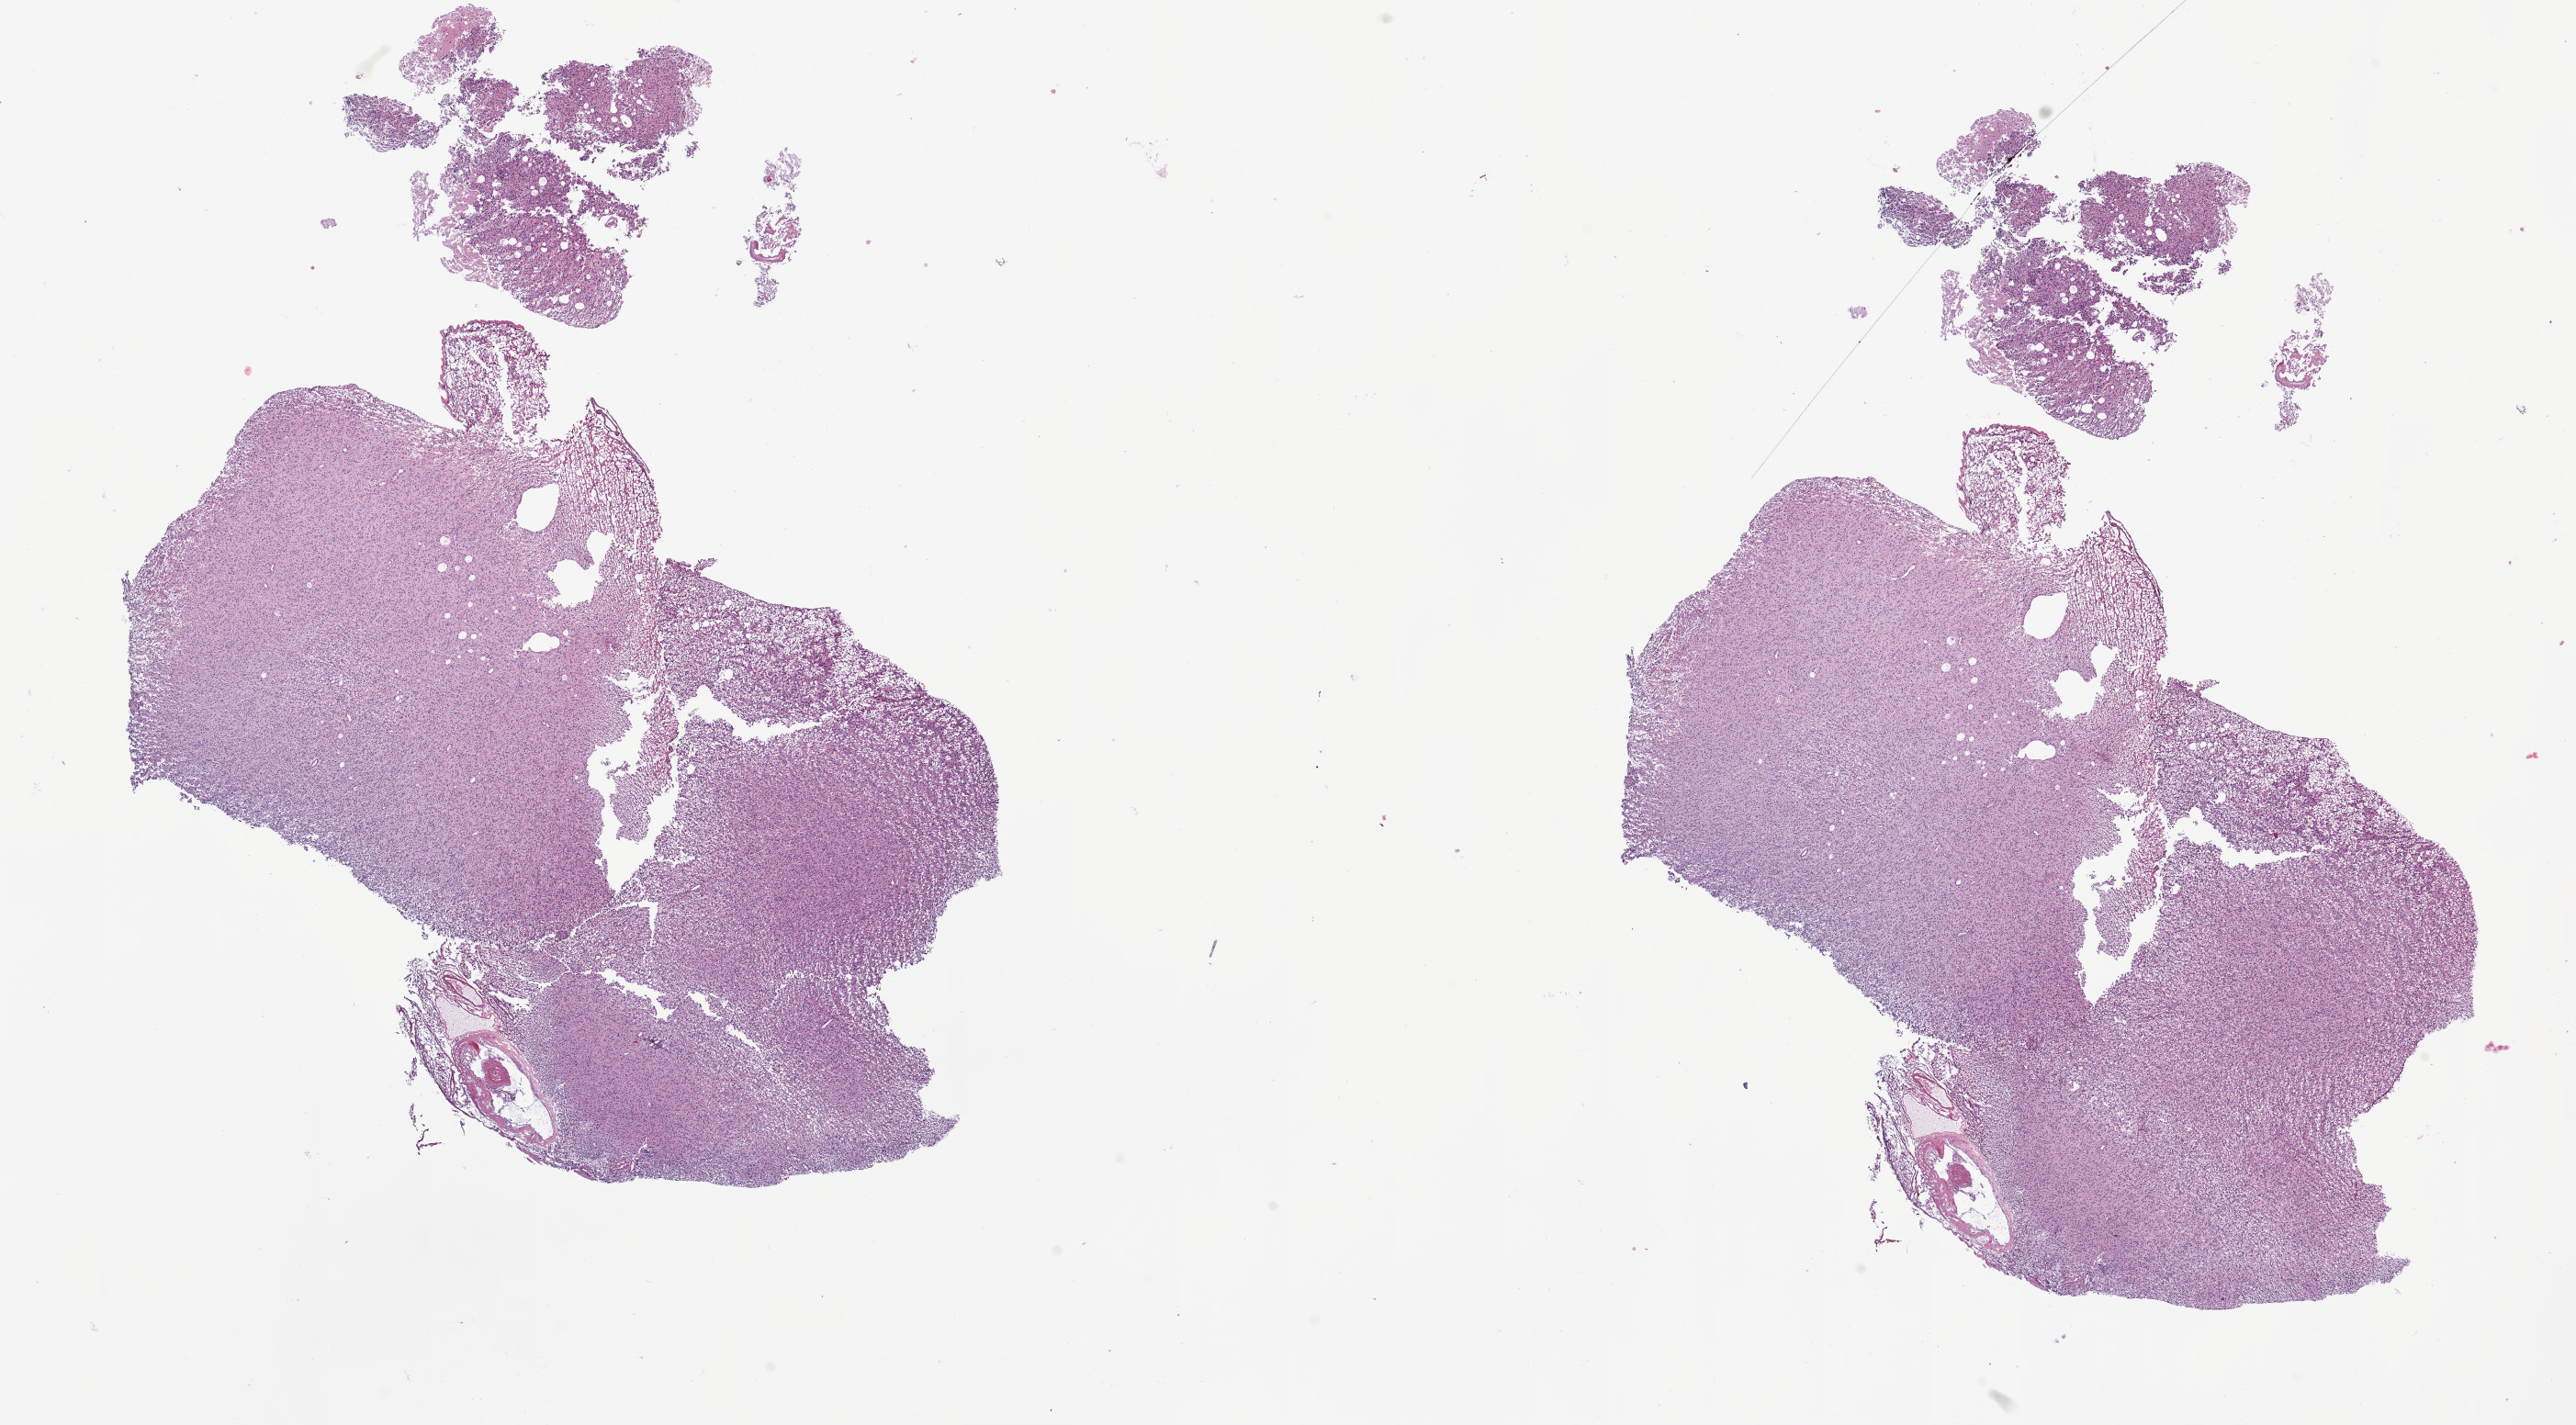
H&E whole-slide image — whole scanned area (about 22.5 x 12.4 mm, from a 5x scan) shown as a low-resolution overview; frozen section; sample: primary tumour, brain. Patient: male, age at initial diagnosis 60 years. Slide review estimates, as recorded: tumour cells 100%, tumour nuclei 80%.
Pathologic diagnosis: Glioblastoma.